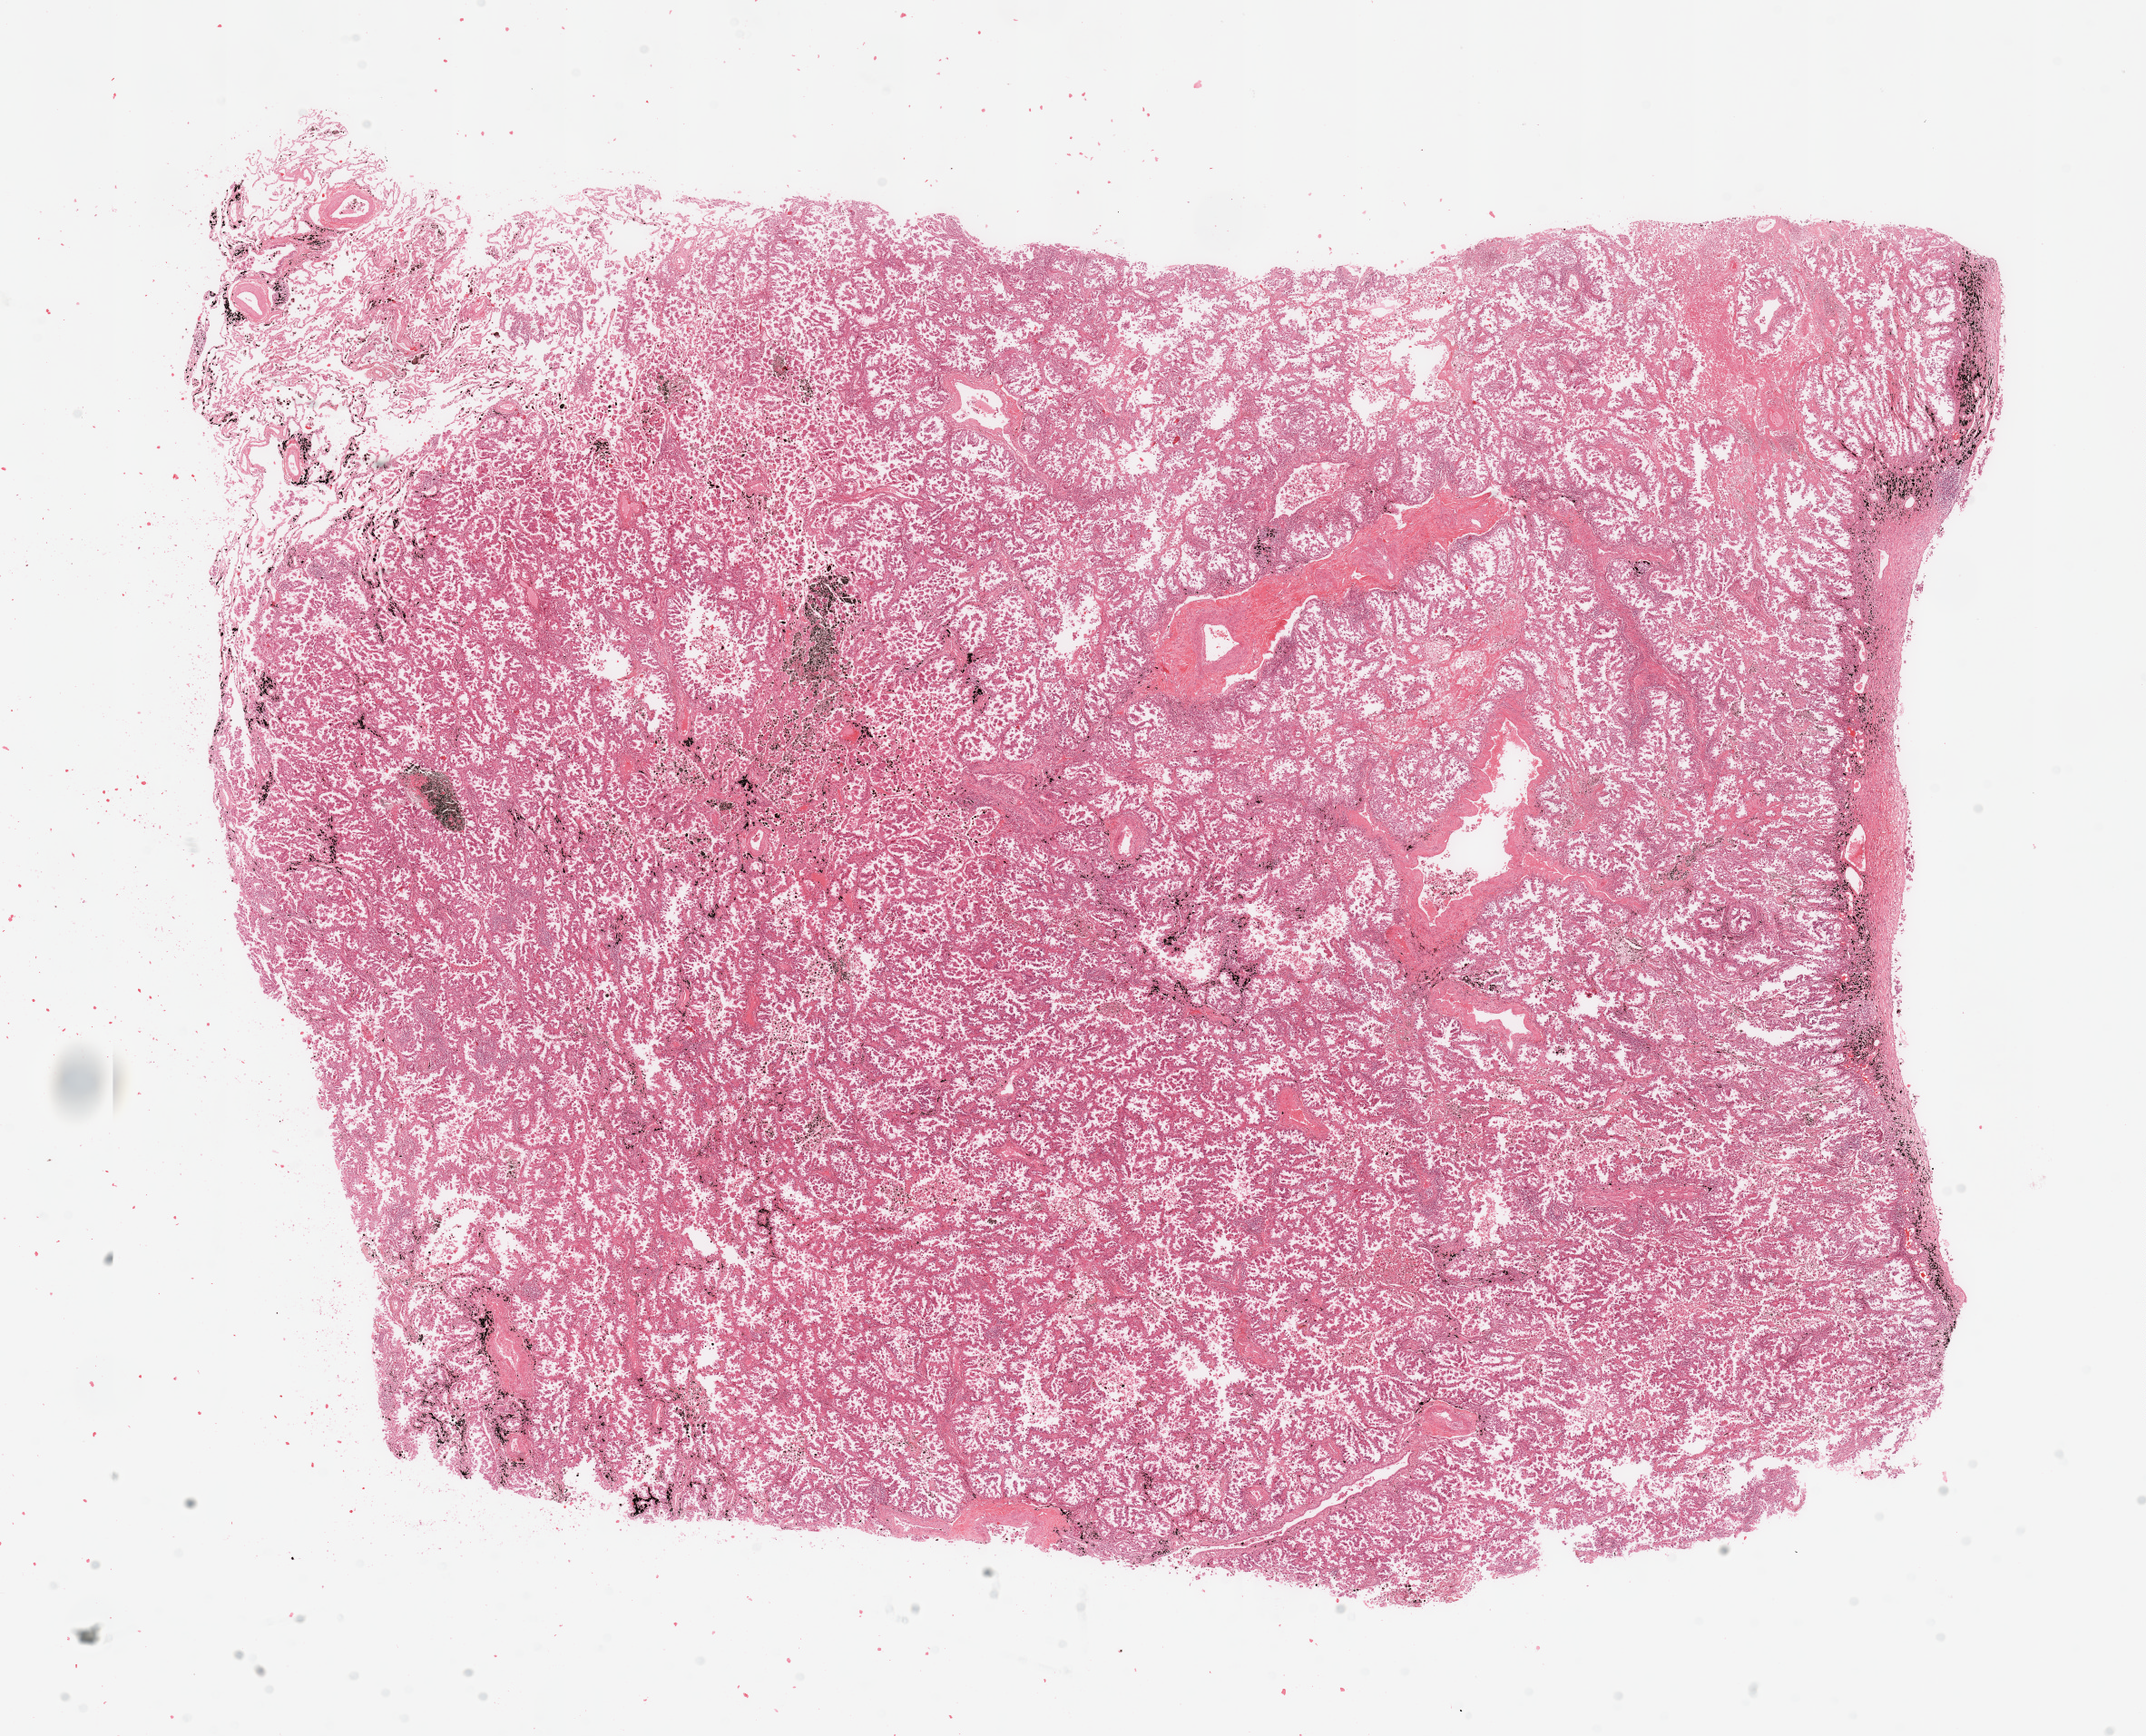
H&E-stained whole-slide image — shown as a low-resolution overview of the whole scanned area (about 18.7 x 15.1 mm). Tumour tissue sample, sampled site: lung. Male, 72 y/o. Slide review estimates, as recorded: tumour nuclei 75%, necrosis 10%.
Histologic diagnosis: Adenocarcinoma, NOS.